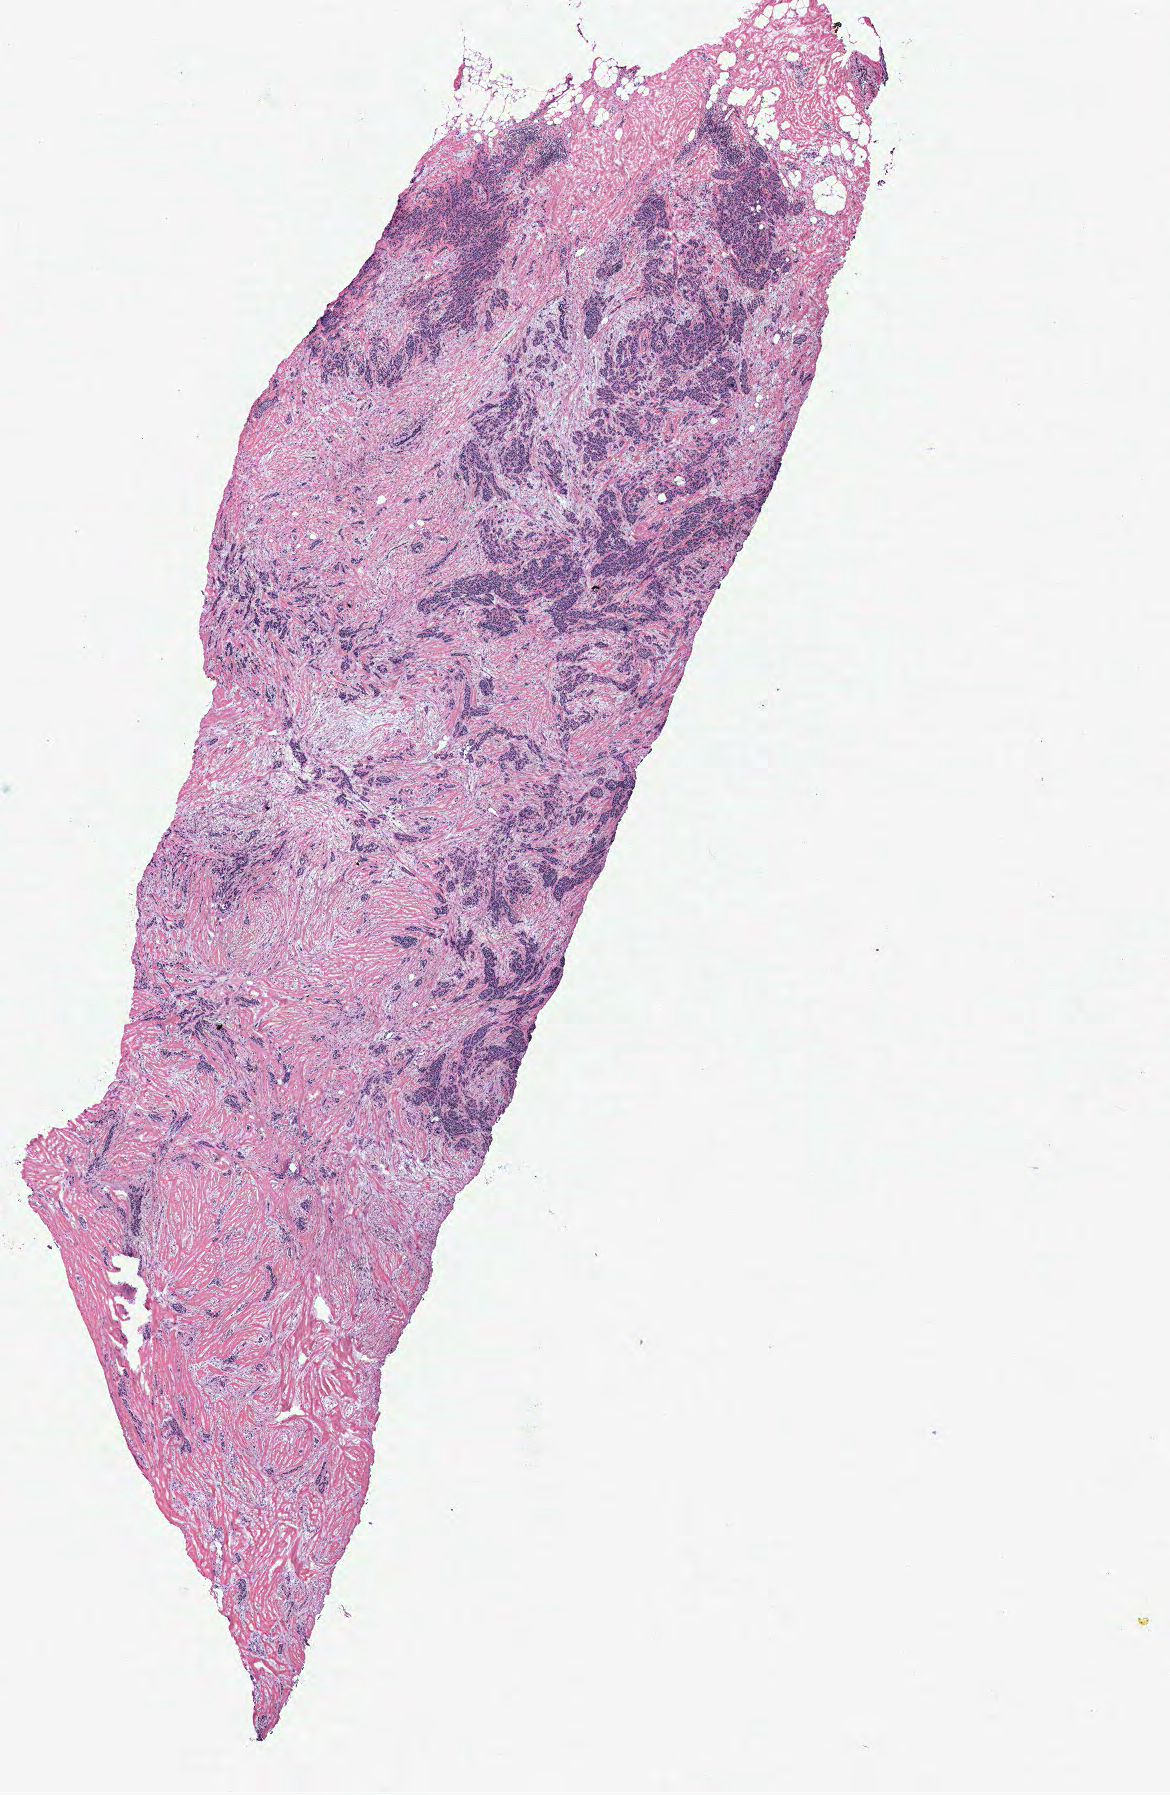
Whole-slide histology image, H&E, shown as a low-resolution overview of the whole scanned area (about 9.4 x 14.4 mm, slide scanned at 40x), breast, tumour tissue. 52-year-old female patient.
AJCC pathologic stage: IIA. Histologic diagnosis: Infiltrating duct carcinoma, NOS.